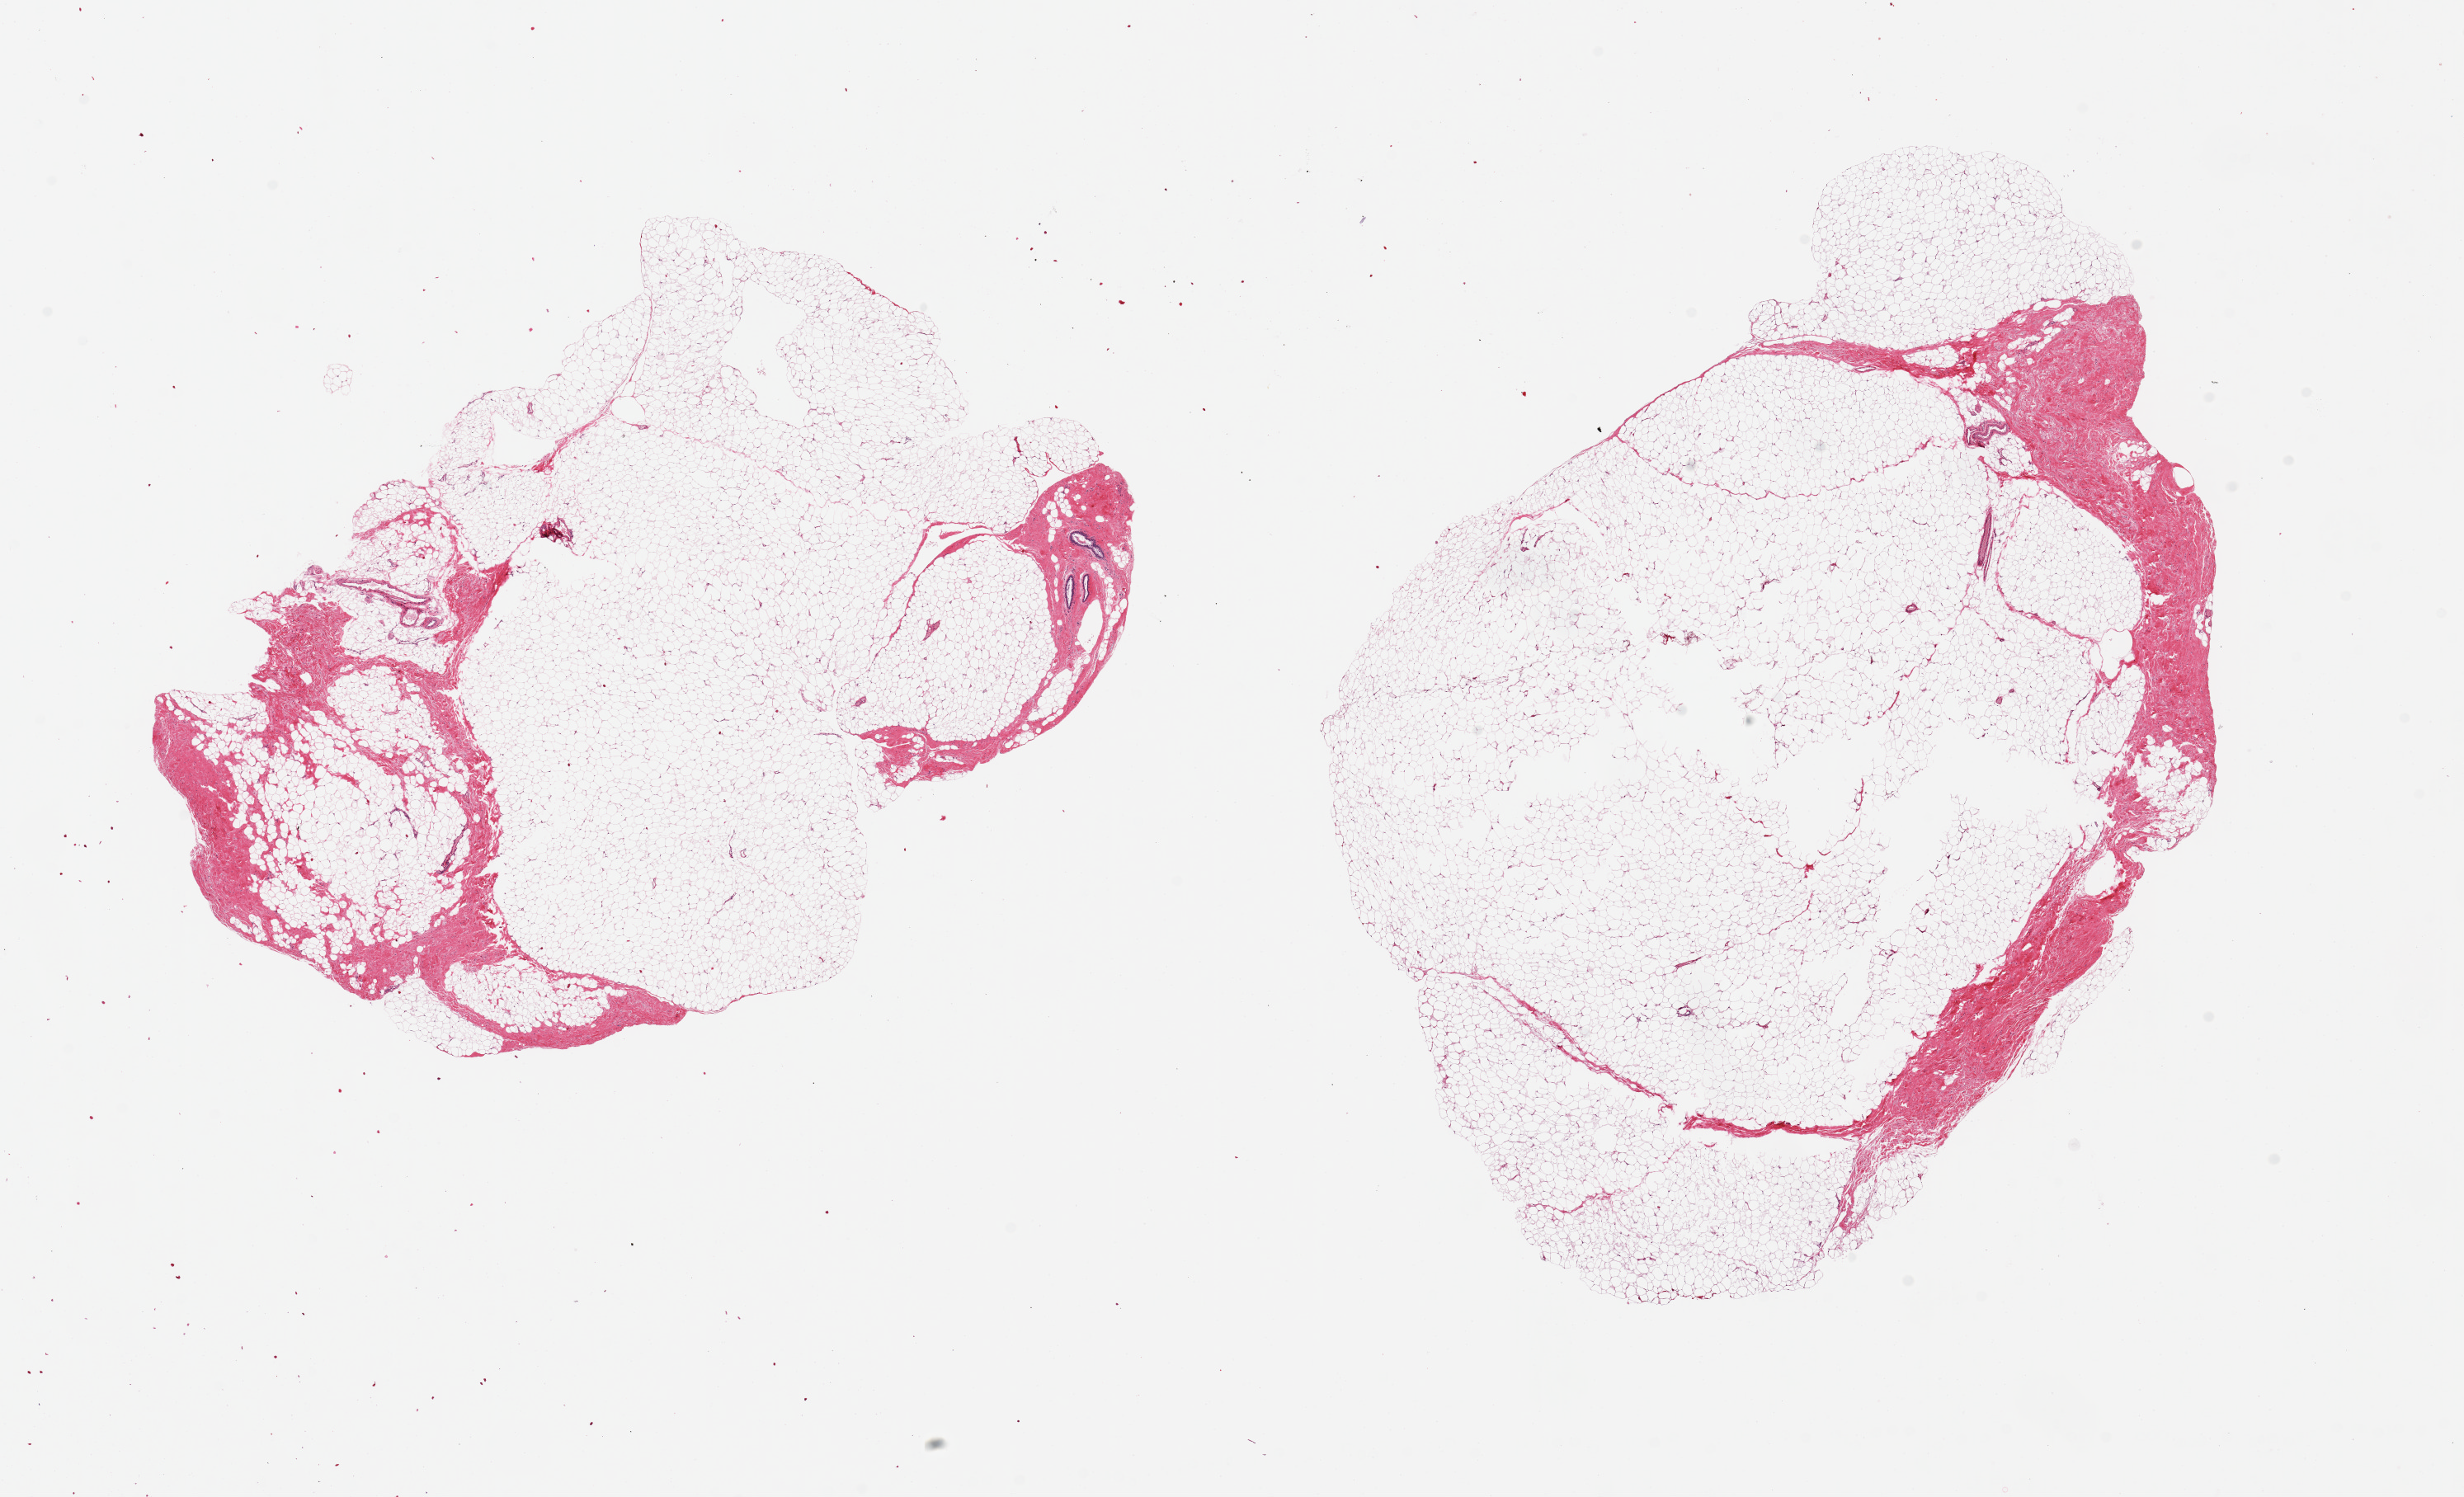
Digitized hematoxylin and eosin (H&E)-stained section, a low-resolution overview of the entire scanned area, about 23.6 x 14.4 mm. PAXgene-fixed paraffin-embedded (PFPE) section. Sampled site (target tissue): breast. Donor tissue sample. Male donor.
* reviewer comment on this tissue sample: 2 pieces, 9x6 & 11x7mm; rare ductal elements